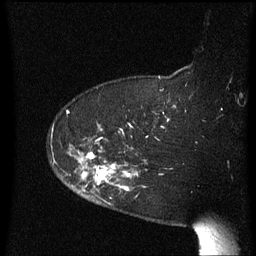
Breast MRI (dynamic contrast-enhanced), one sagittal slice. Position 49 of 60 along the scan axis. Dynamic contrast-enhanced series, image 2 of 3 at this slice position (ordered by acquisition). 1.5 T. TE 4.2 ms, TR 8.4 ms. 2.3 mm slice thickness. 256 × 256 image matrix. Patient: female, 63 years. Case-level facts recorded for this patient, not image findings: setting: breast cancer imaged before/during neoadjuvant chemotherapy; receptor status: HER2-positive.
Annotated regions visible in this slice (semi-automatically segmented with operator editing):
- analysis volume of interest (the breast-tissue region the enhancement analysis was run in; not a lesion): bounding box <63,144,147,205> (left, top, right, bottom; pixels)
- tumour enhancement mask (voxels above the 70 % enhancement threshold inside the analysis volume of interest): <81,153,130,190>